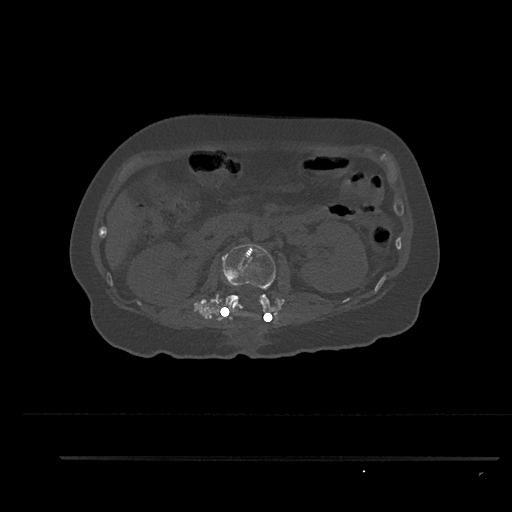
CT including the spine, one axial slice. Slice 182 of 797 in the series (ordered by position). Reconstruction kernel Br40s/3. 120 kVp. Bone window (W 1800 / L 400 HU). 0.5 mm slice thickness. 512 × 512 image matrix. Female patient, age 44 years. From the clinical record (not read from this slice): primary cancer: renal; vertebrae with lytic lesions (as recorded): L1.
Annotated regions visible in this slice (semi-automatically segmented with operator editing):
- L2 vertebra: bounding box <224,244,276,320> (left, top, right, bottom; pixels)